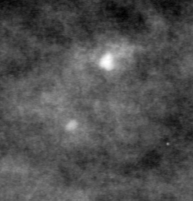
Cropped region of a digitized screen-film mammogram centred on a radiologist-marked abnormality, right breast, MLO view, BI-RADS breast density category 3 (scale 1–4).
Marked abnormality: calcifications, morphology pleomorphic, distribution clustered; BI-RADS assessment category 4; pathology (as recorded): malignant.